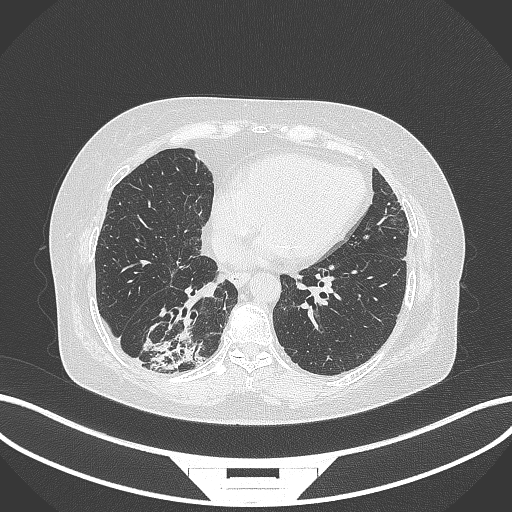
Chest CT, one axial slice. Slice 78 of 296 in the series (ordered by position). Reconstruction kernel B70f. 120 kVp. Lung window (W 1500 / L -600 HU). 512 × 512 image matrix, field of view 400 × 400 mm. Patient: female, 65 years. From the clinical record (not read from this slice): clinical TNM (as recorded): T2b N1 M0; histopathological grade: G1.
Structures marked on this image (rectangle marked by the reading radiologist):
- lung tumour (recorded histology: adenocarcinoma): bounding box [x1, y1, x2, y2] px = [140, 316, 212, 376]